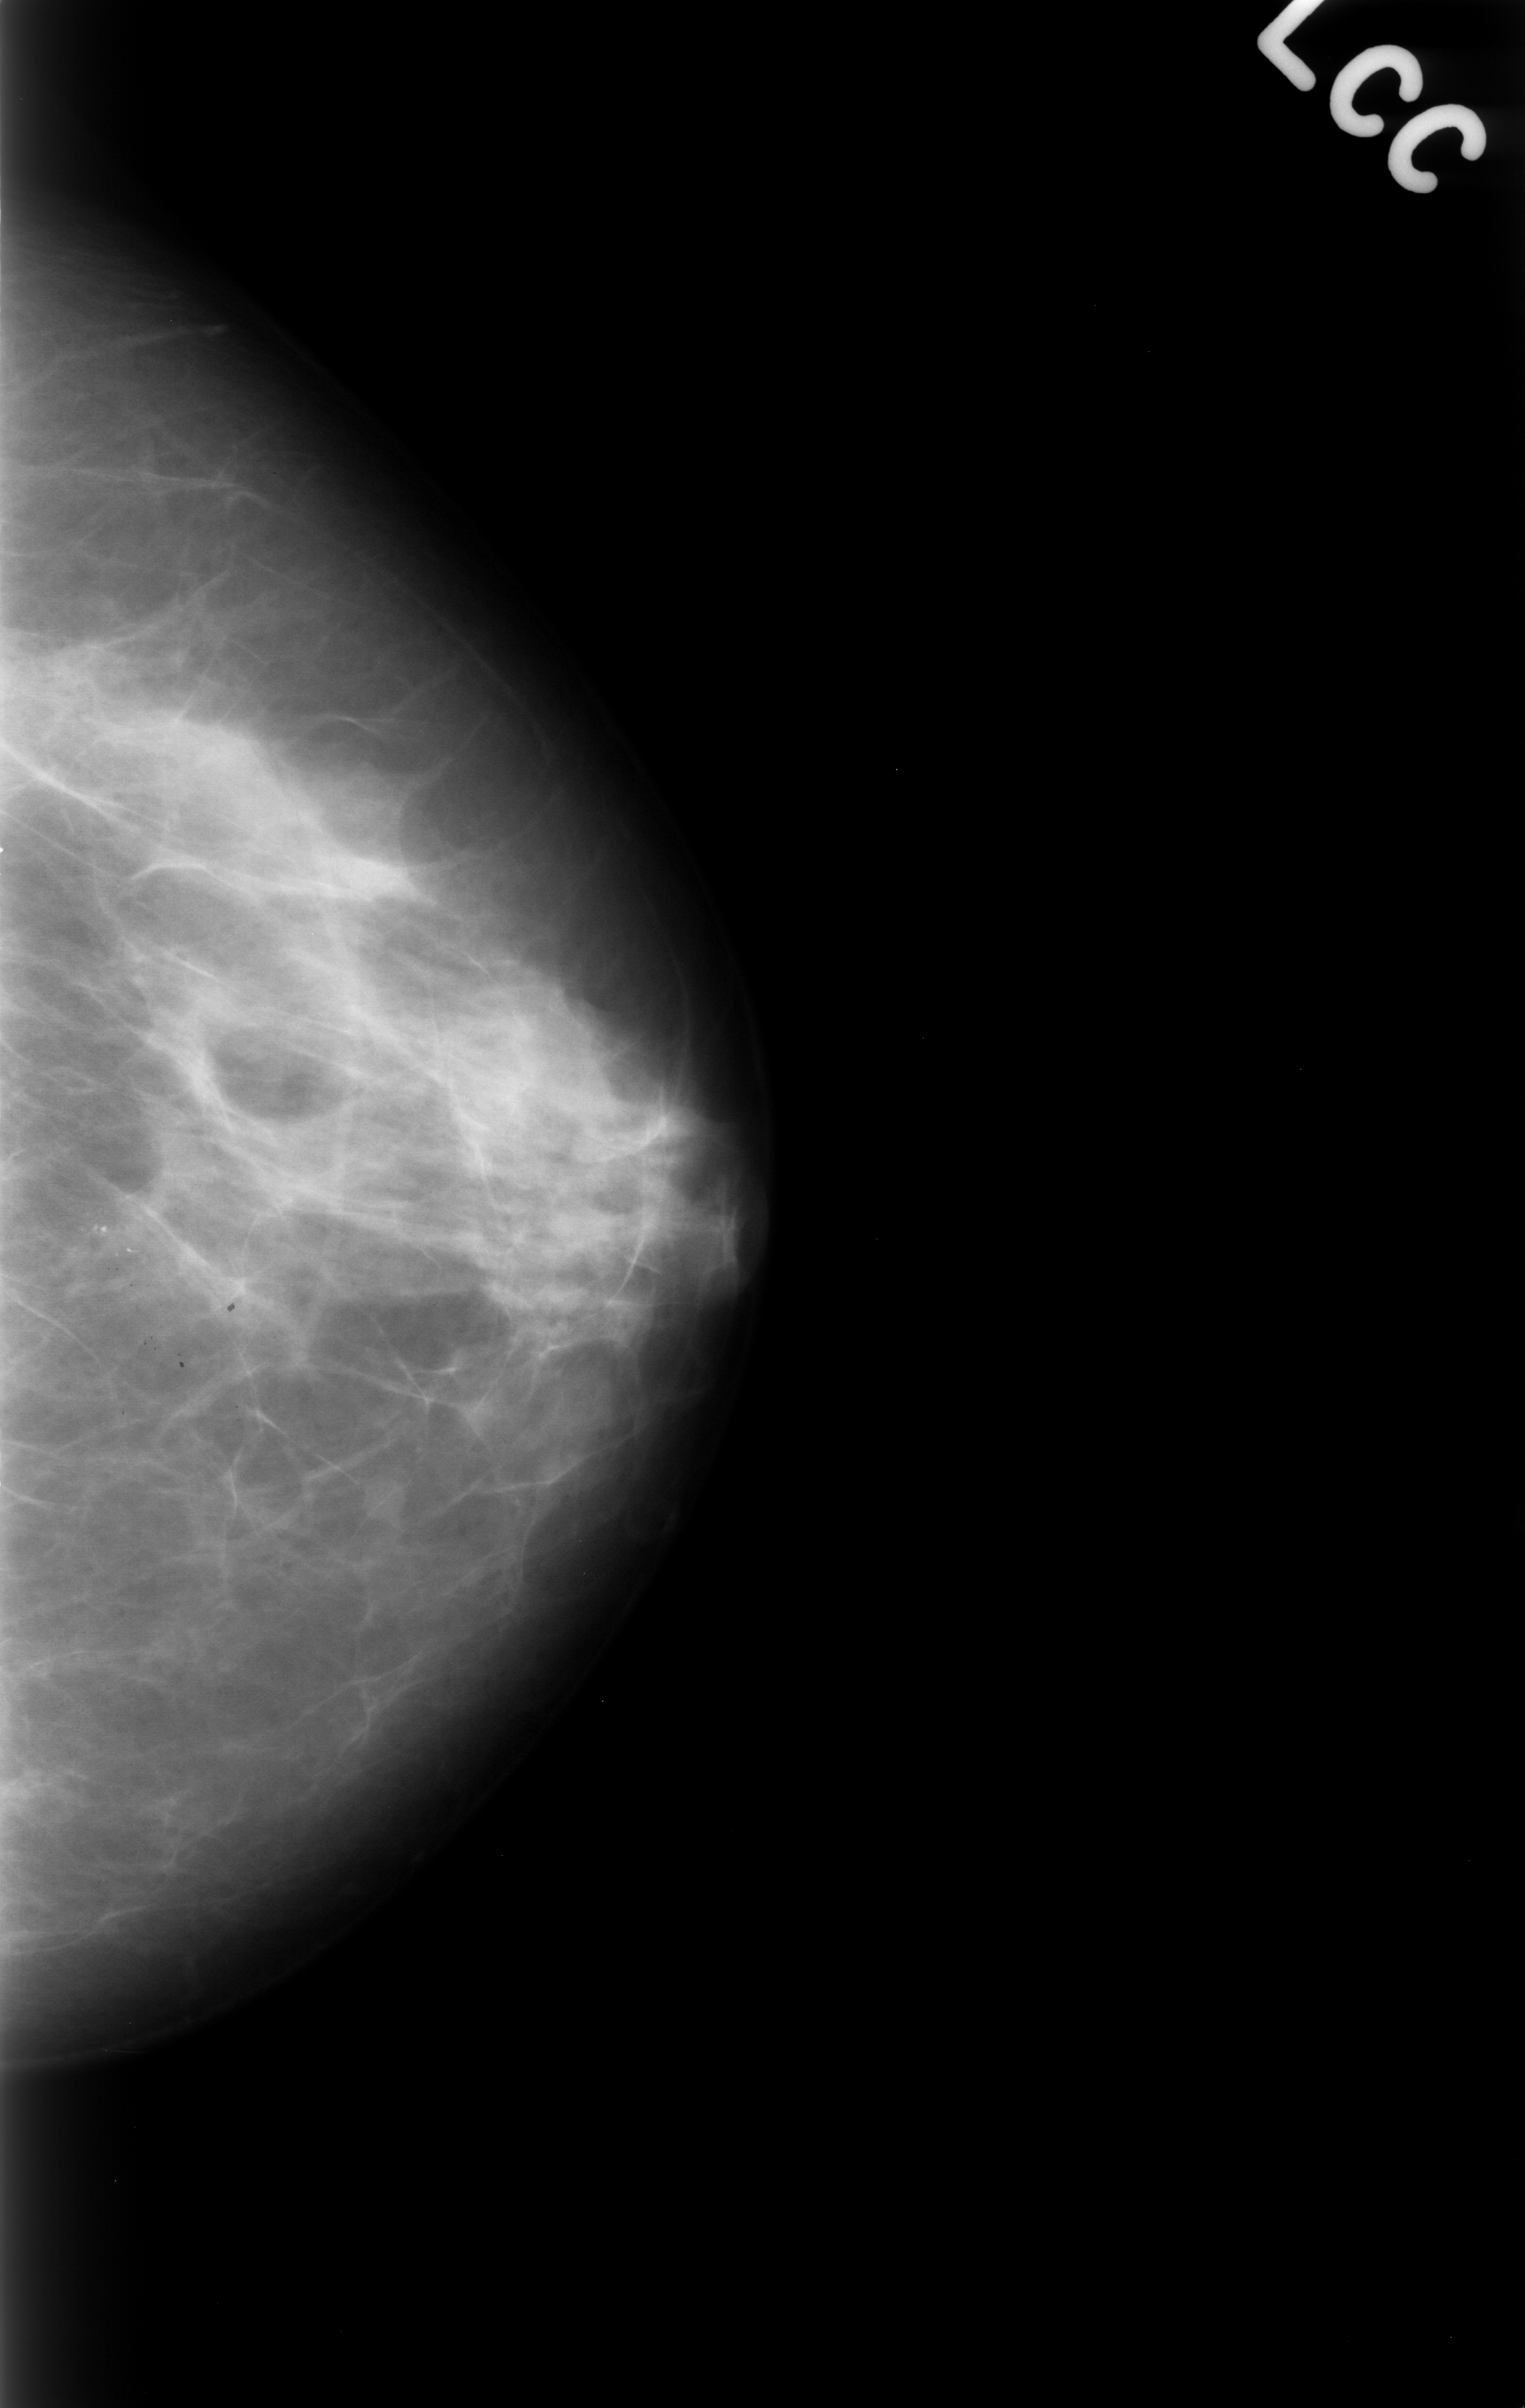
Digitized screen-film mammogram, left breast, craniocaudal (CC) view, breast composition: scattered fibroglandular densities (BI-RADS density category 2 of 4).
- Radiologist-marked abnormalities on this image: calcifications, morphology punctate, distribution clustered; BI-RADS assessment category 4; subtlety rating 4 on a 1 (subtle) to 5 (obvious) scale; pathology (as recorded): benign.